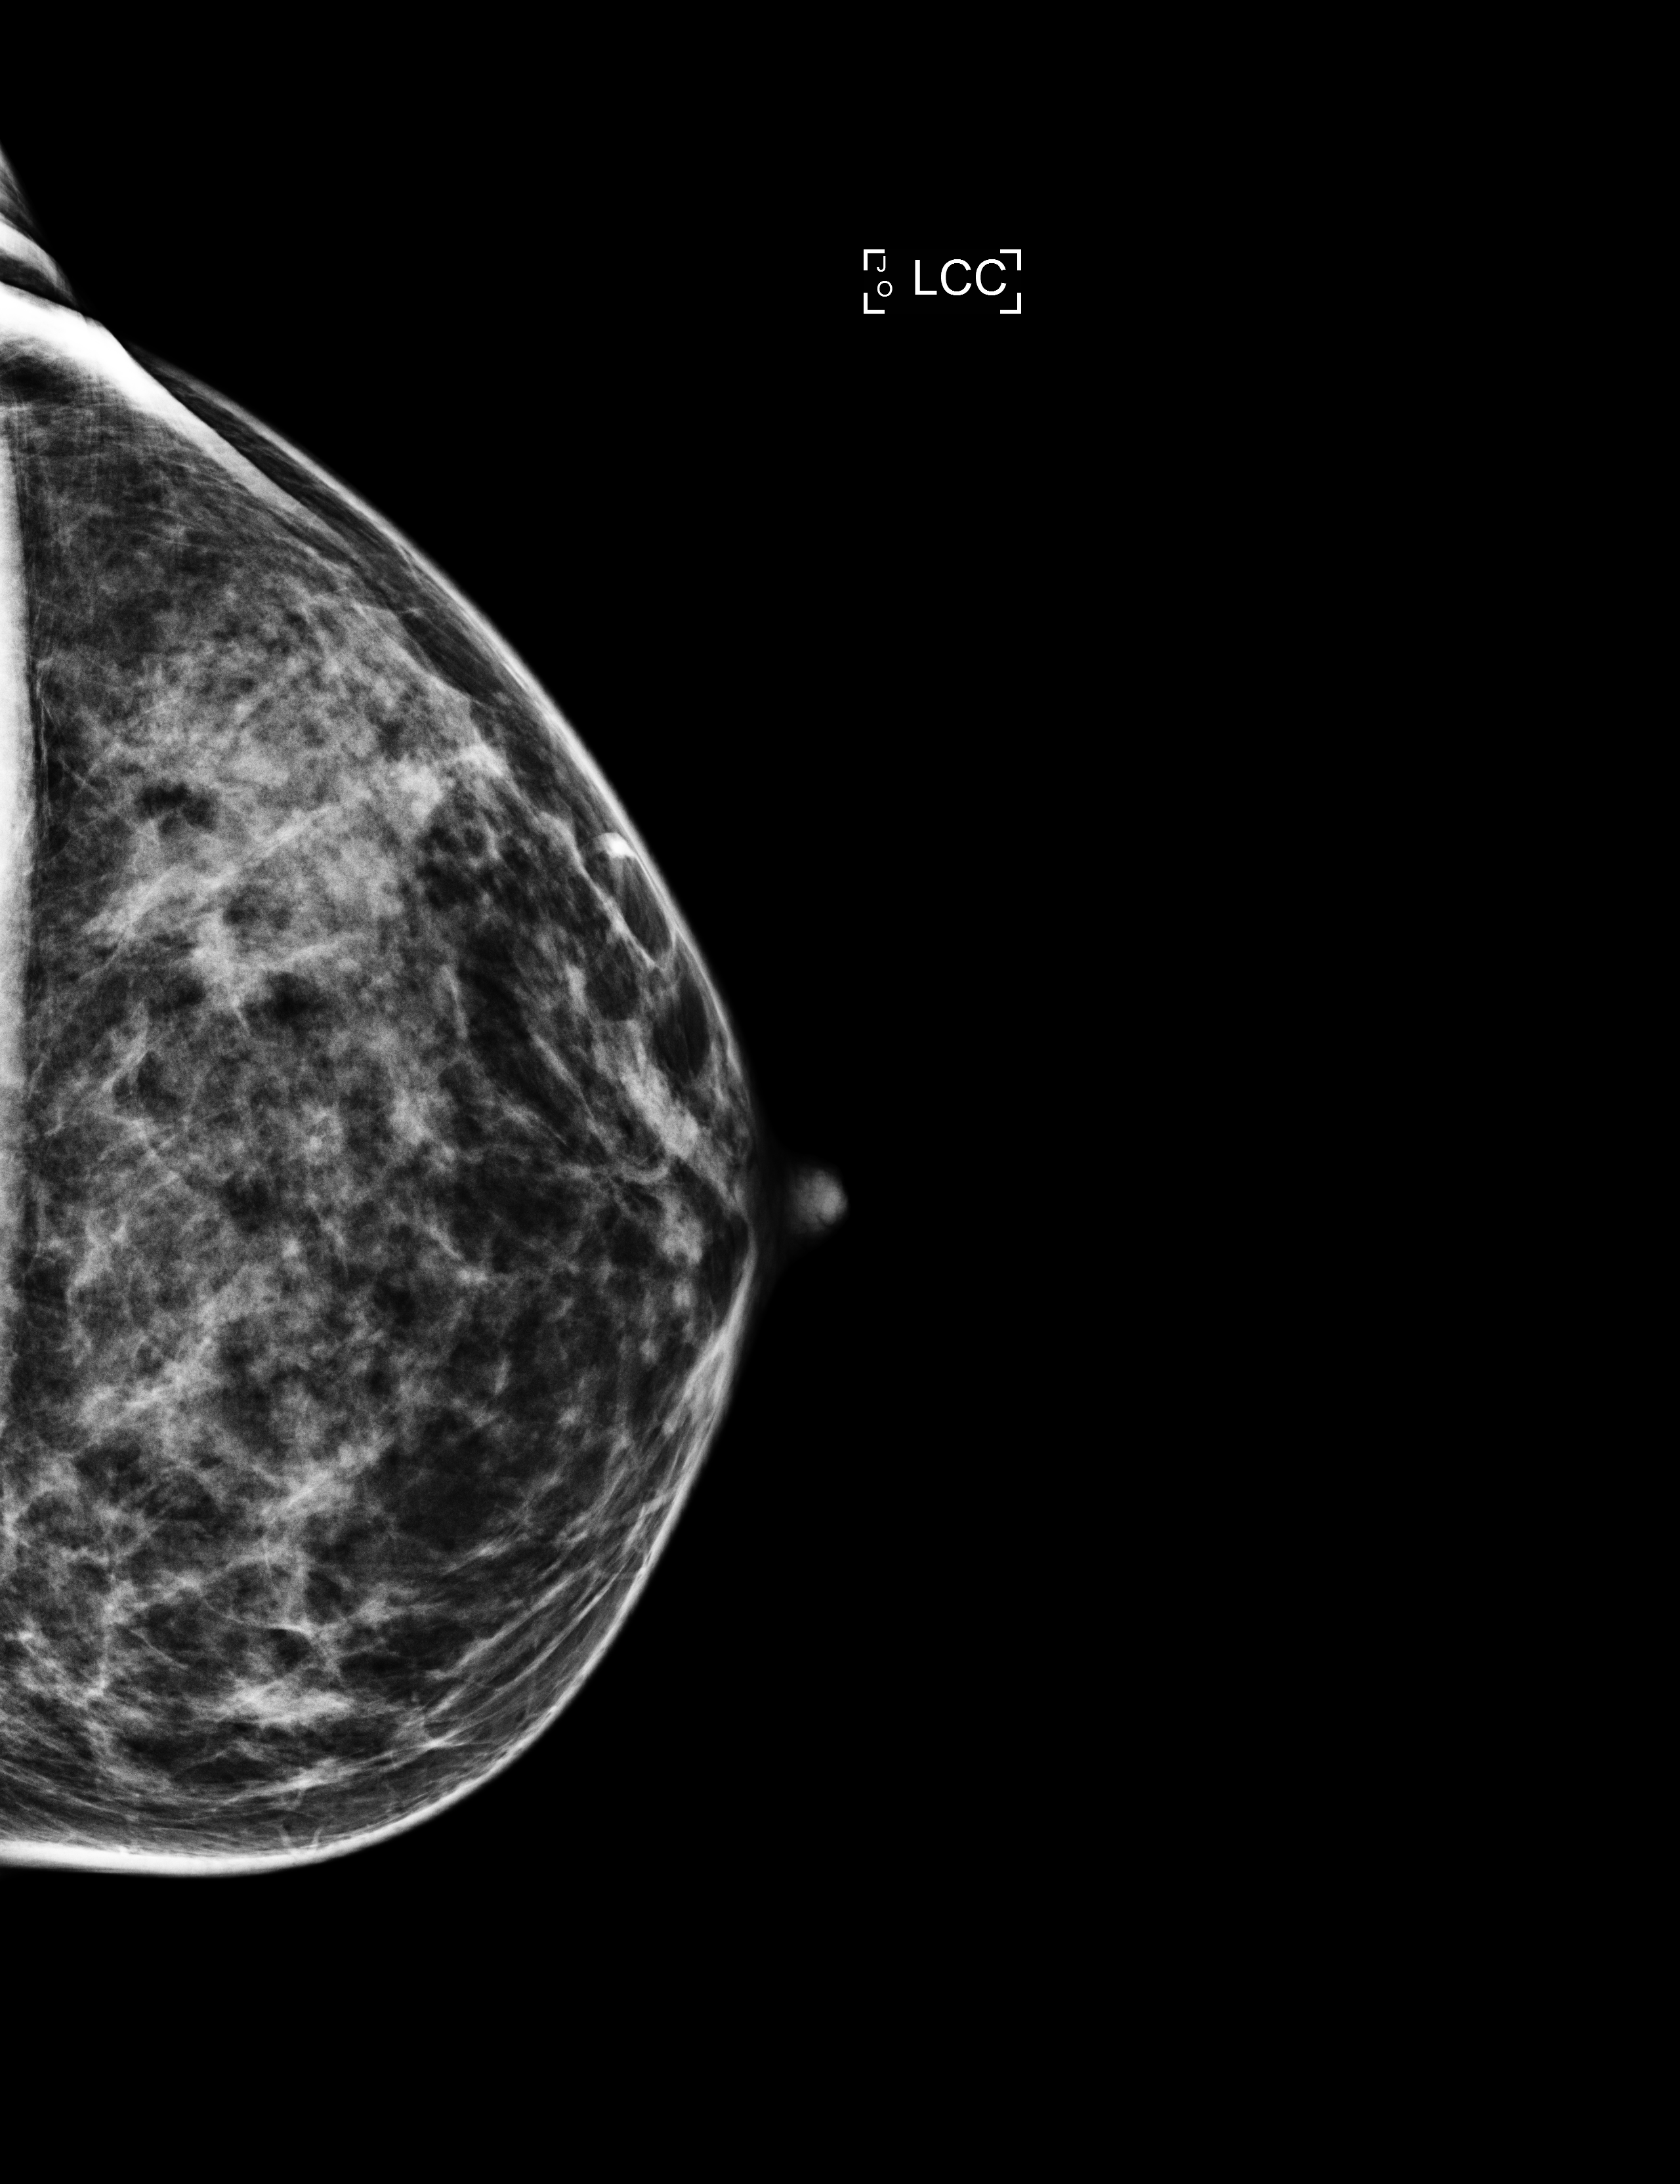
Full-field digital mammogram (FFDM); left breast; CC view; annual screening mammography examination; compressed breast thickness 53 mm. Patient: female, 41 years.
Breast density at the screening exam (both breasts): heterogeneously dense (BI-RADS density category c). Final BI-RADS category for the screening round (tomosynthesis exam, both breasts): category 1. Recall: no recall after this screen.